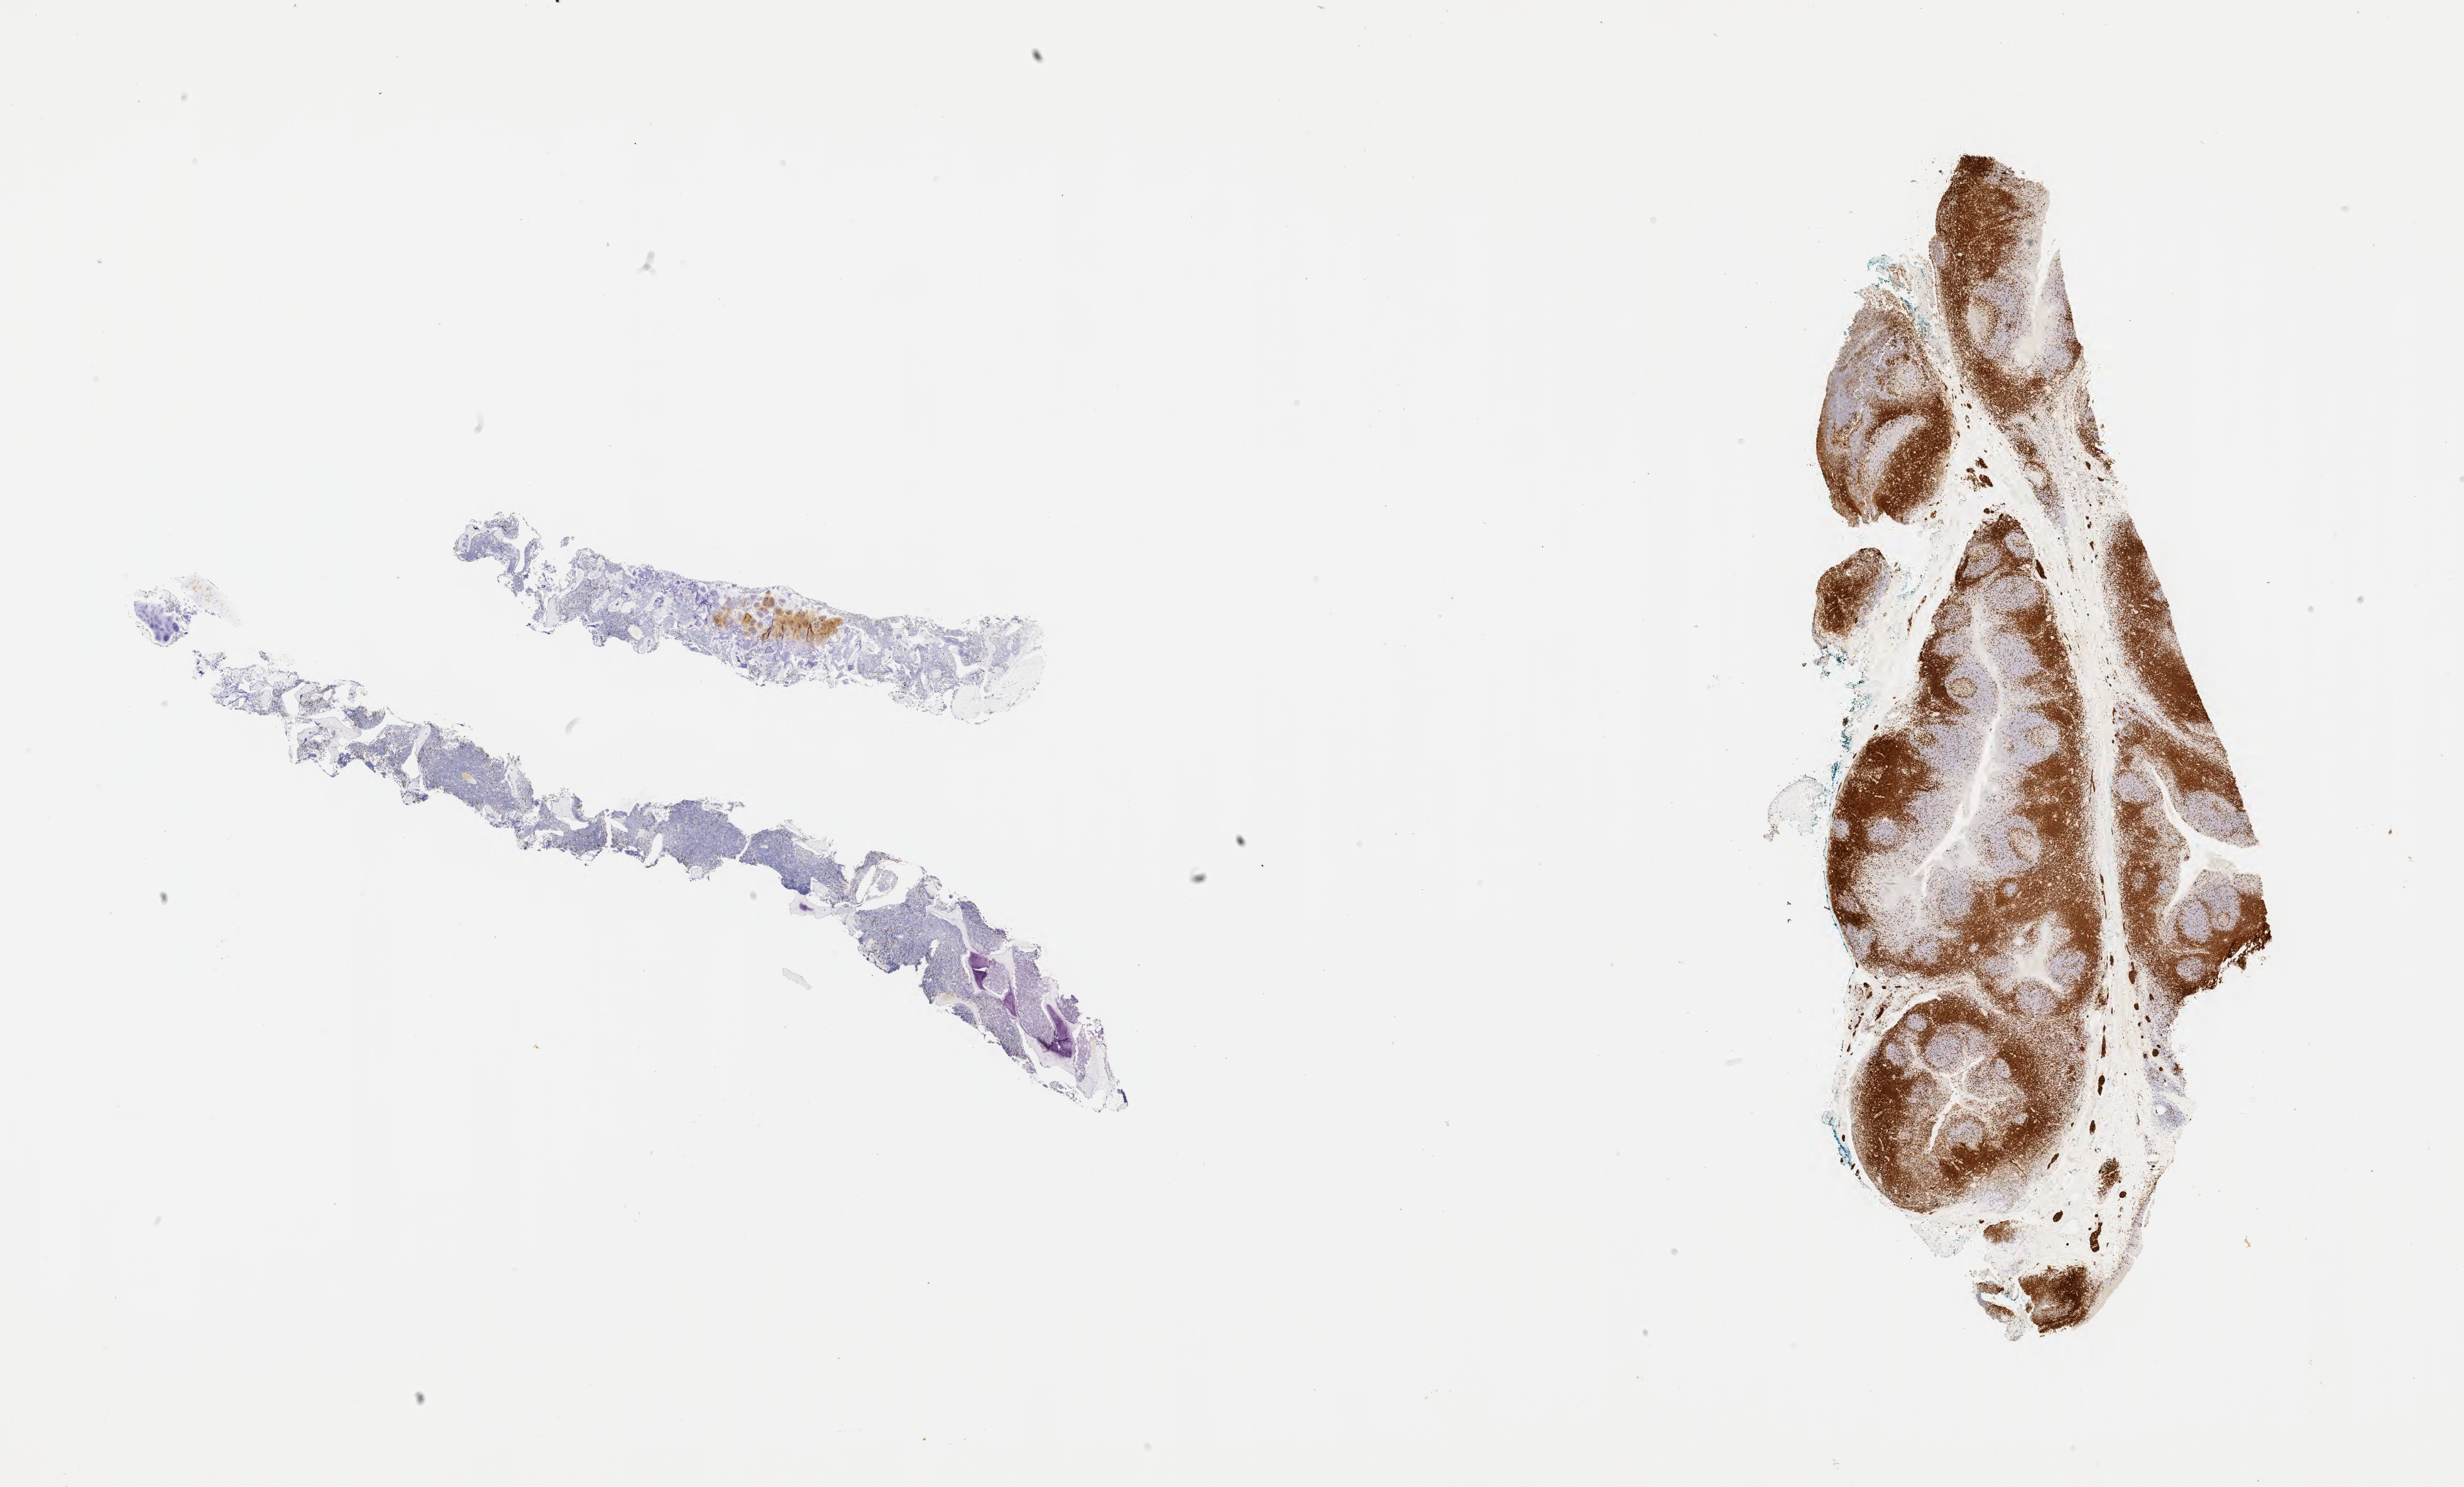
IHC for CD3, whole-slide image — whole scanned area (about 31.7 x 19.1 mm) shown as a low-resolution overview. Tumor tissue. Anatomic site: bone marrow. Patient male; age 11 years.
Histologic diagnosis: Burkitt lymphoma, NOS.